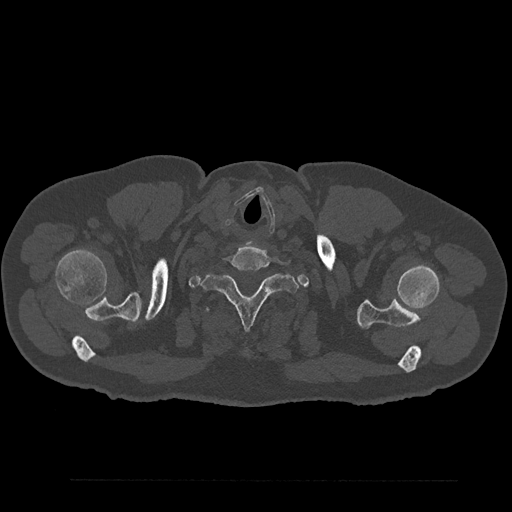
CT including the spine, one axial slice. Position 756 of 797 along the scan axis. Reconstruction kernel Br40s/3. Bone window (W 1800 / L 400 HU). 0.5 mm slice thickness. 512 × 512 image matrix, field of view 430 × 430 mm. Male patient, age 61 years. From the clinical record (not read from this slice): primary cancer: prostate.
Structures marked on this image (semi-automatic segmentation, software-assisted and operator-edited):
- T1 vertebra: bounding box (x1, y1, x2, y2) in pixels: (201, 274, 298, 330)
- T2 vertebra: (202, 306, 292, 350)